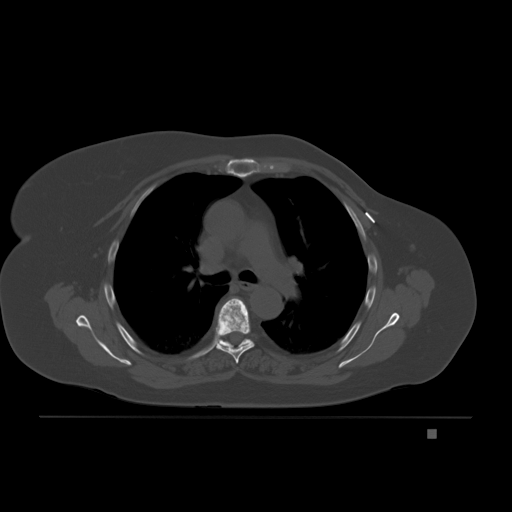
CT including the spine, one axial slice. Position 143 of 221 along the scan axis. Bone window (W 1800 / L 400 HU). 3 mm slice thickness. 512 × 512 image matrix. Patient: female, 63 years. Case-level facts recorded for this patient, not image findings: primary cancer: breast.
Structures marked on this image (semi-automatic segmentation, software-assisted and operator-edited):
- T5 vertebra: bounding box <216,298,255,363> (left, top, right, bottom; pixels)
- T6 vertebra: <222,339,248,345>